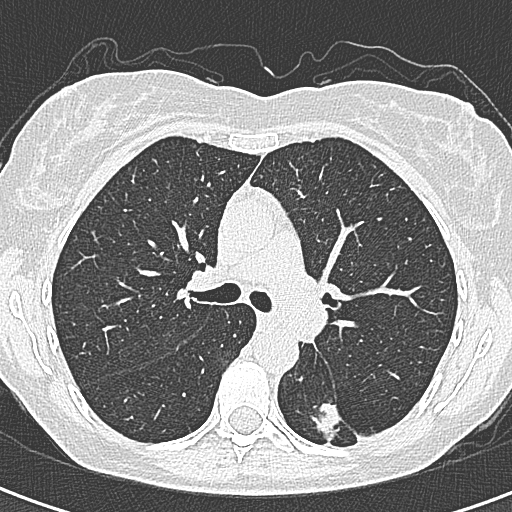
Axial slice from a low-dose chest CT screening exam, first (baseline) screen, lung window (W 1500 / L -600 HU), 1 mm slice thickness, lung (sharp) reconstruction kernel (B80f), slice 118 of 328 in the series. Female, age 58 years at enrolment. Former smoker at enrolment.
- Lesion marked by an expert reader, bounding box [x1, y1, x2, y2] px = [291, 391, 362, 455].
- The screening reader recorded 2 non-calcified nodules or masses ≥4 mm on this exam (left lower lobe, right lower lobe); which of them this box marks is not recorded.